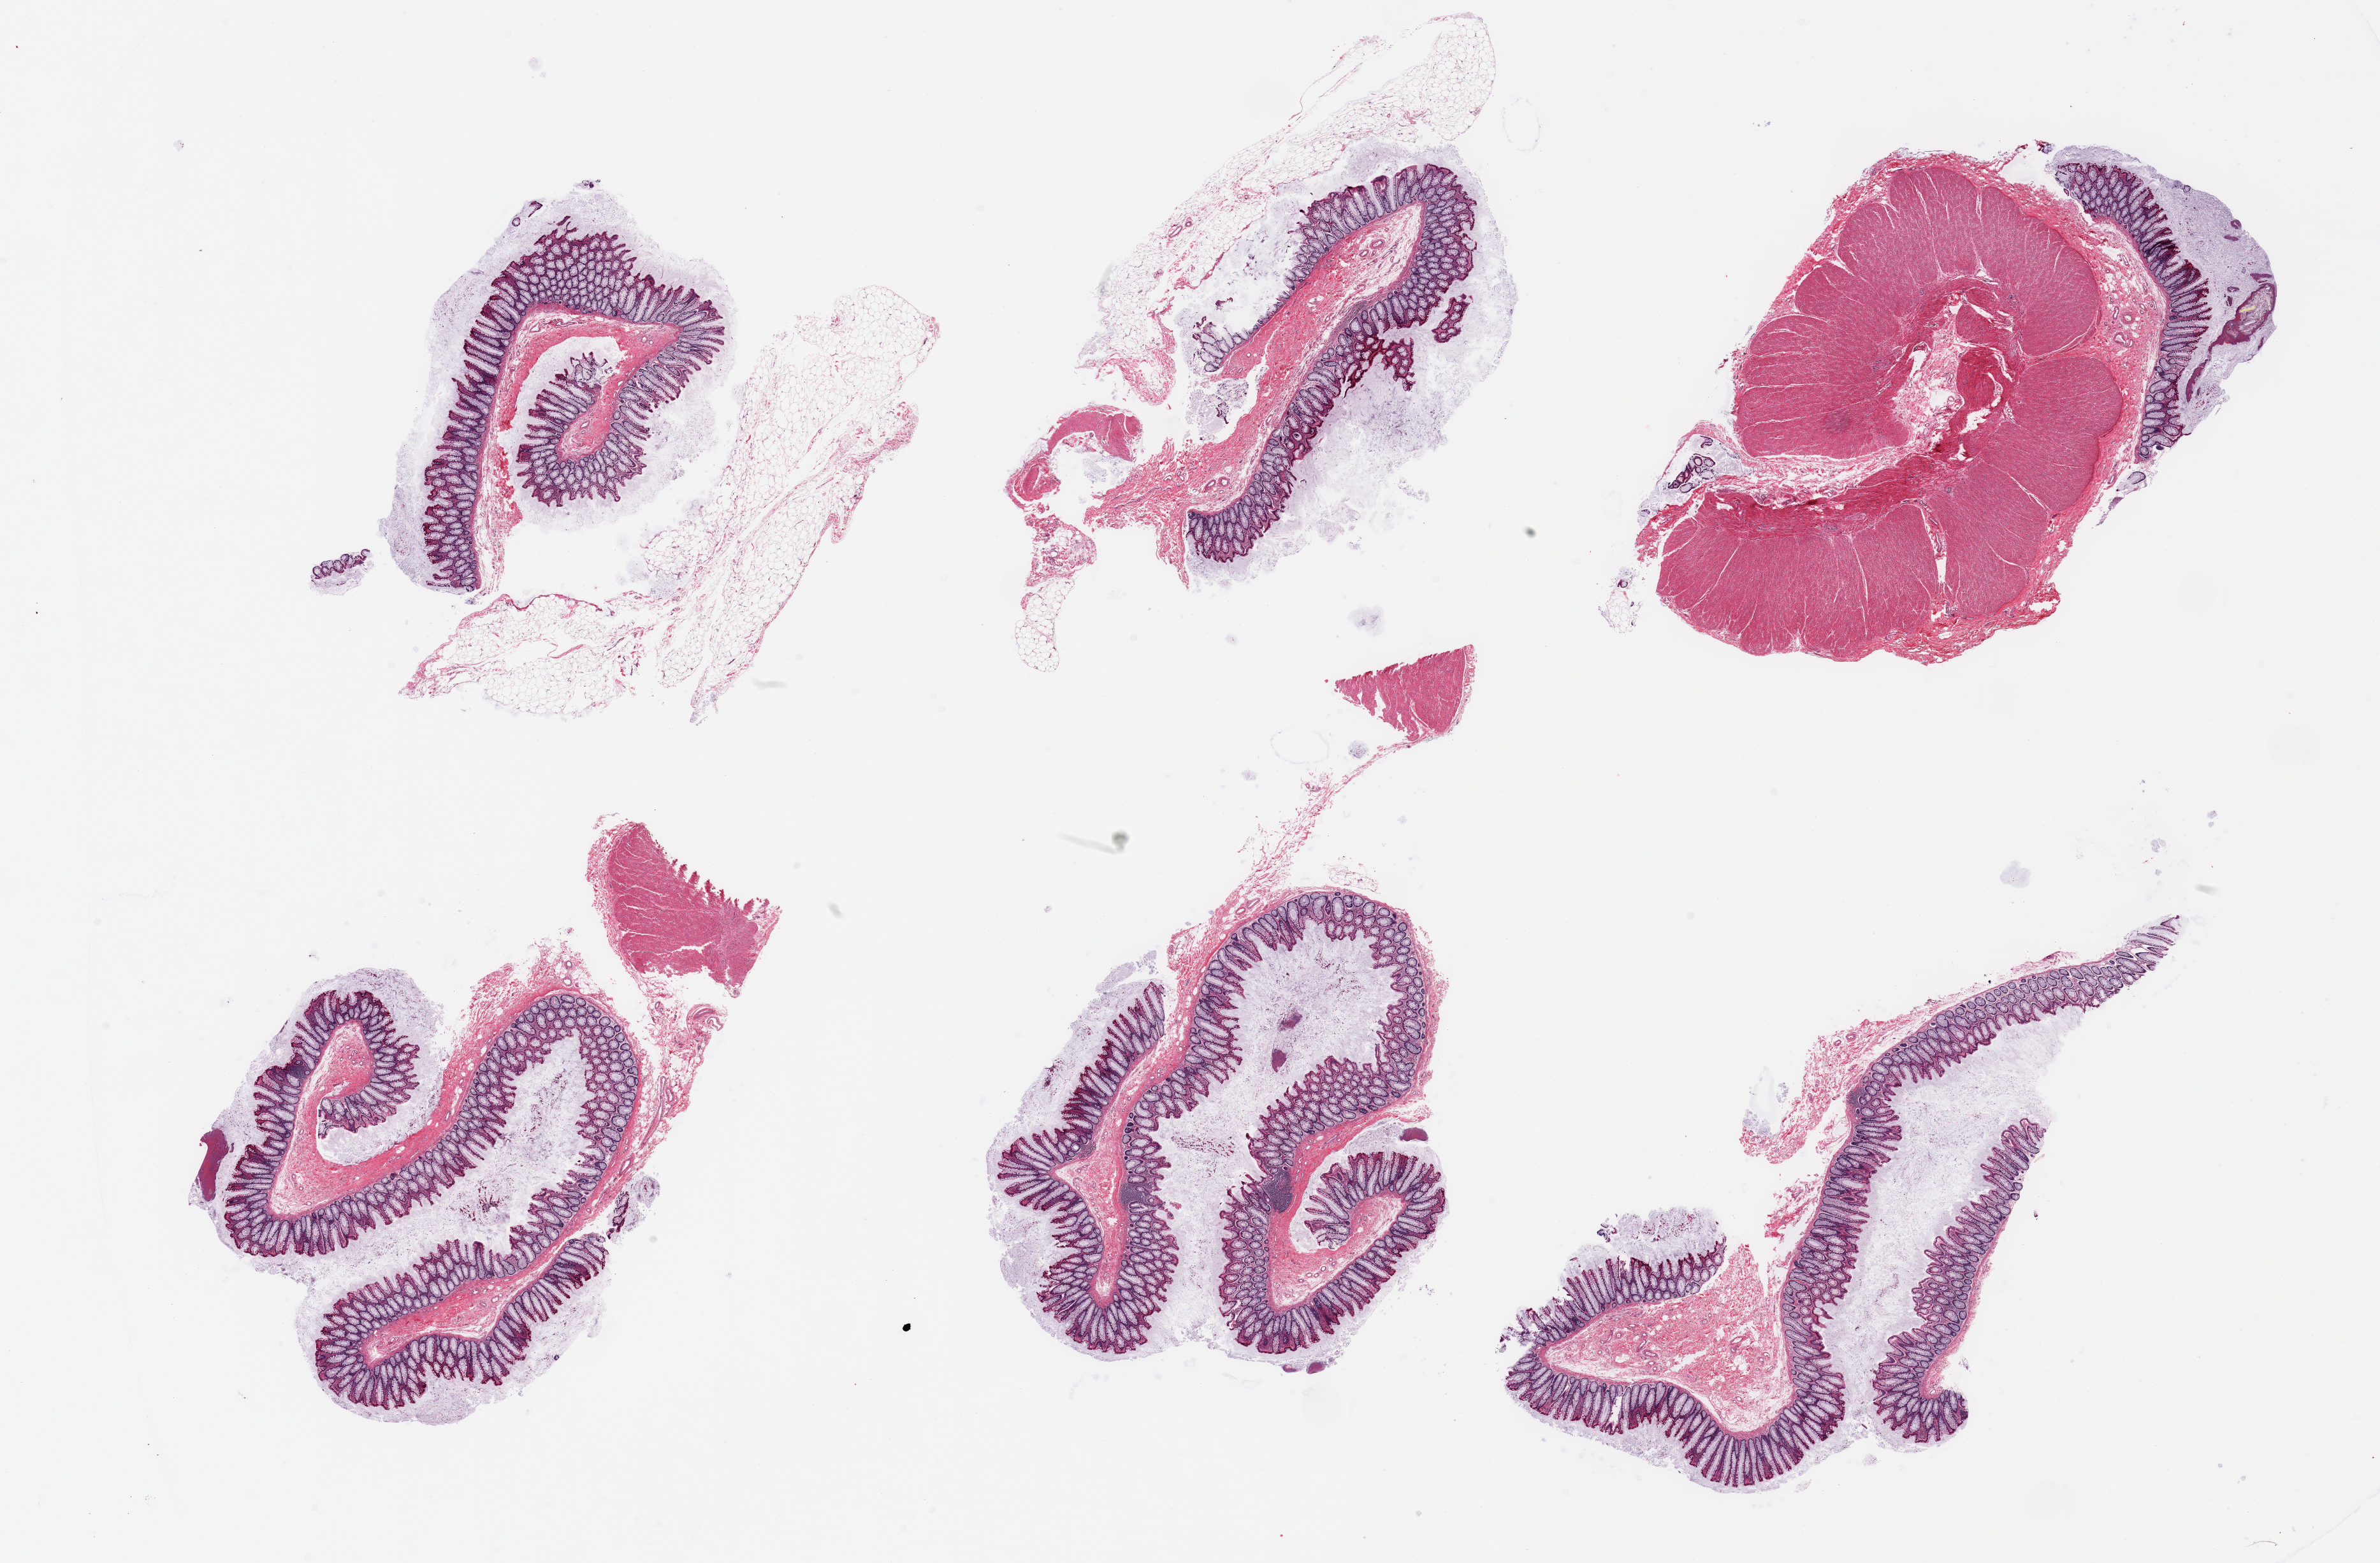
Digitized H&E-stained section — low-resolution overview of the scanned area, about 29.5 x 19.4 mm, PAXgene-fixed, paraffin-embedded tissue, section of sigmoid colon (target tissue), tissue donor sample. Donor: male.
Reviewer comment on this tissue sample: 6 pieces; predominantly mucosa (not target), with small proportion of muscularis.